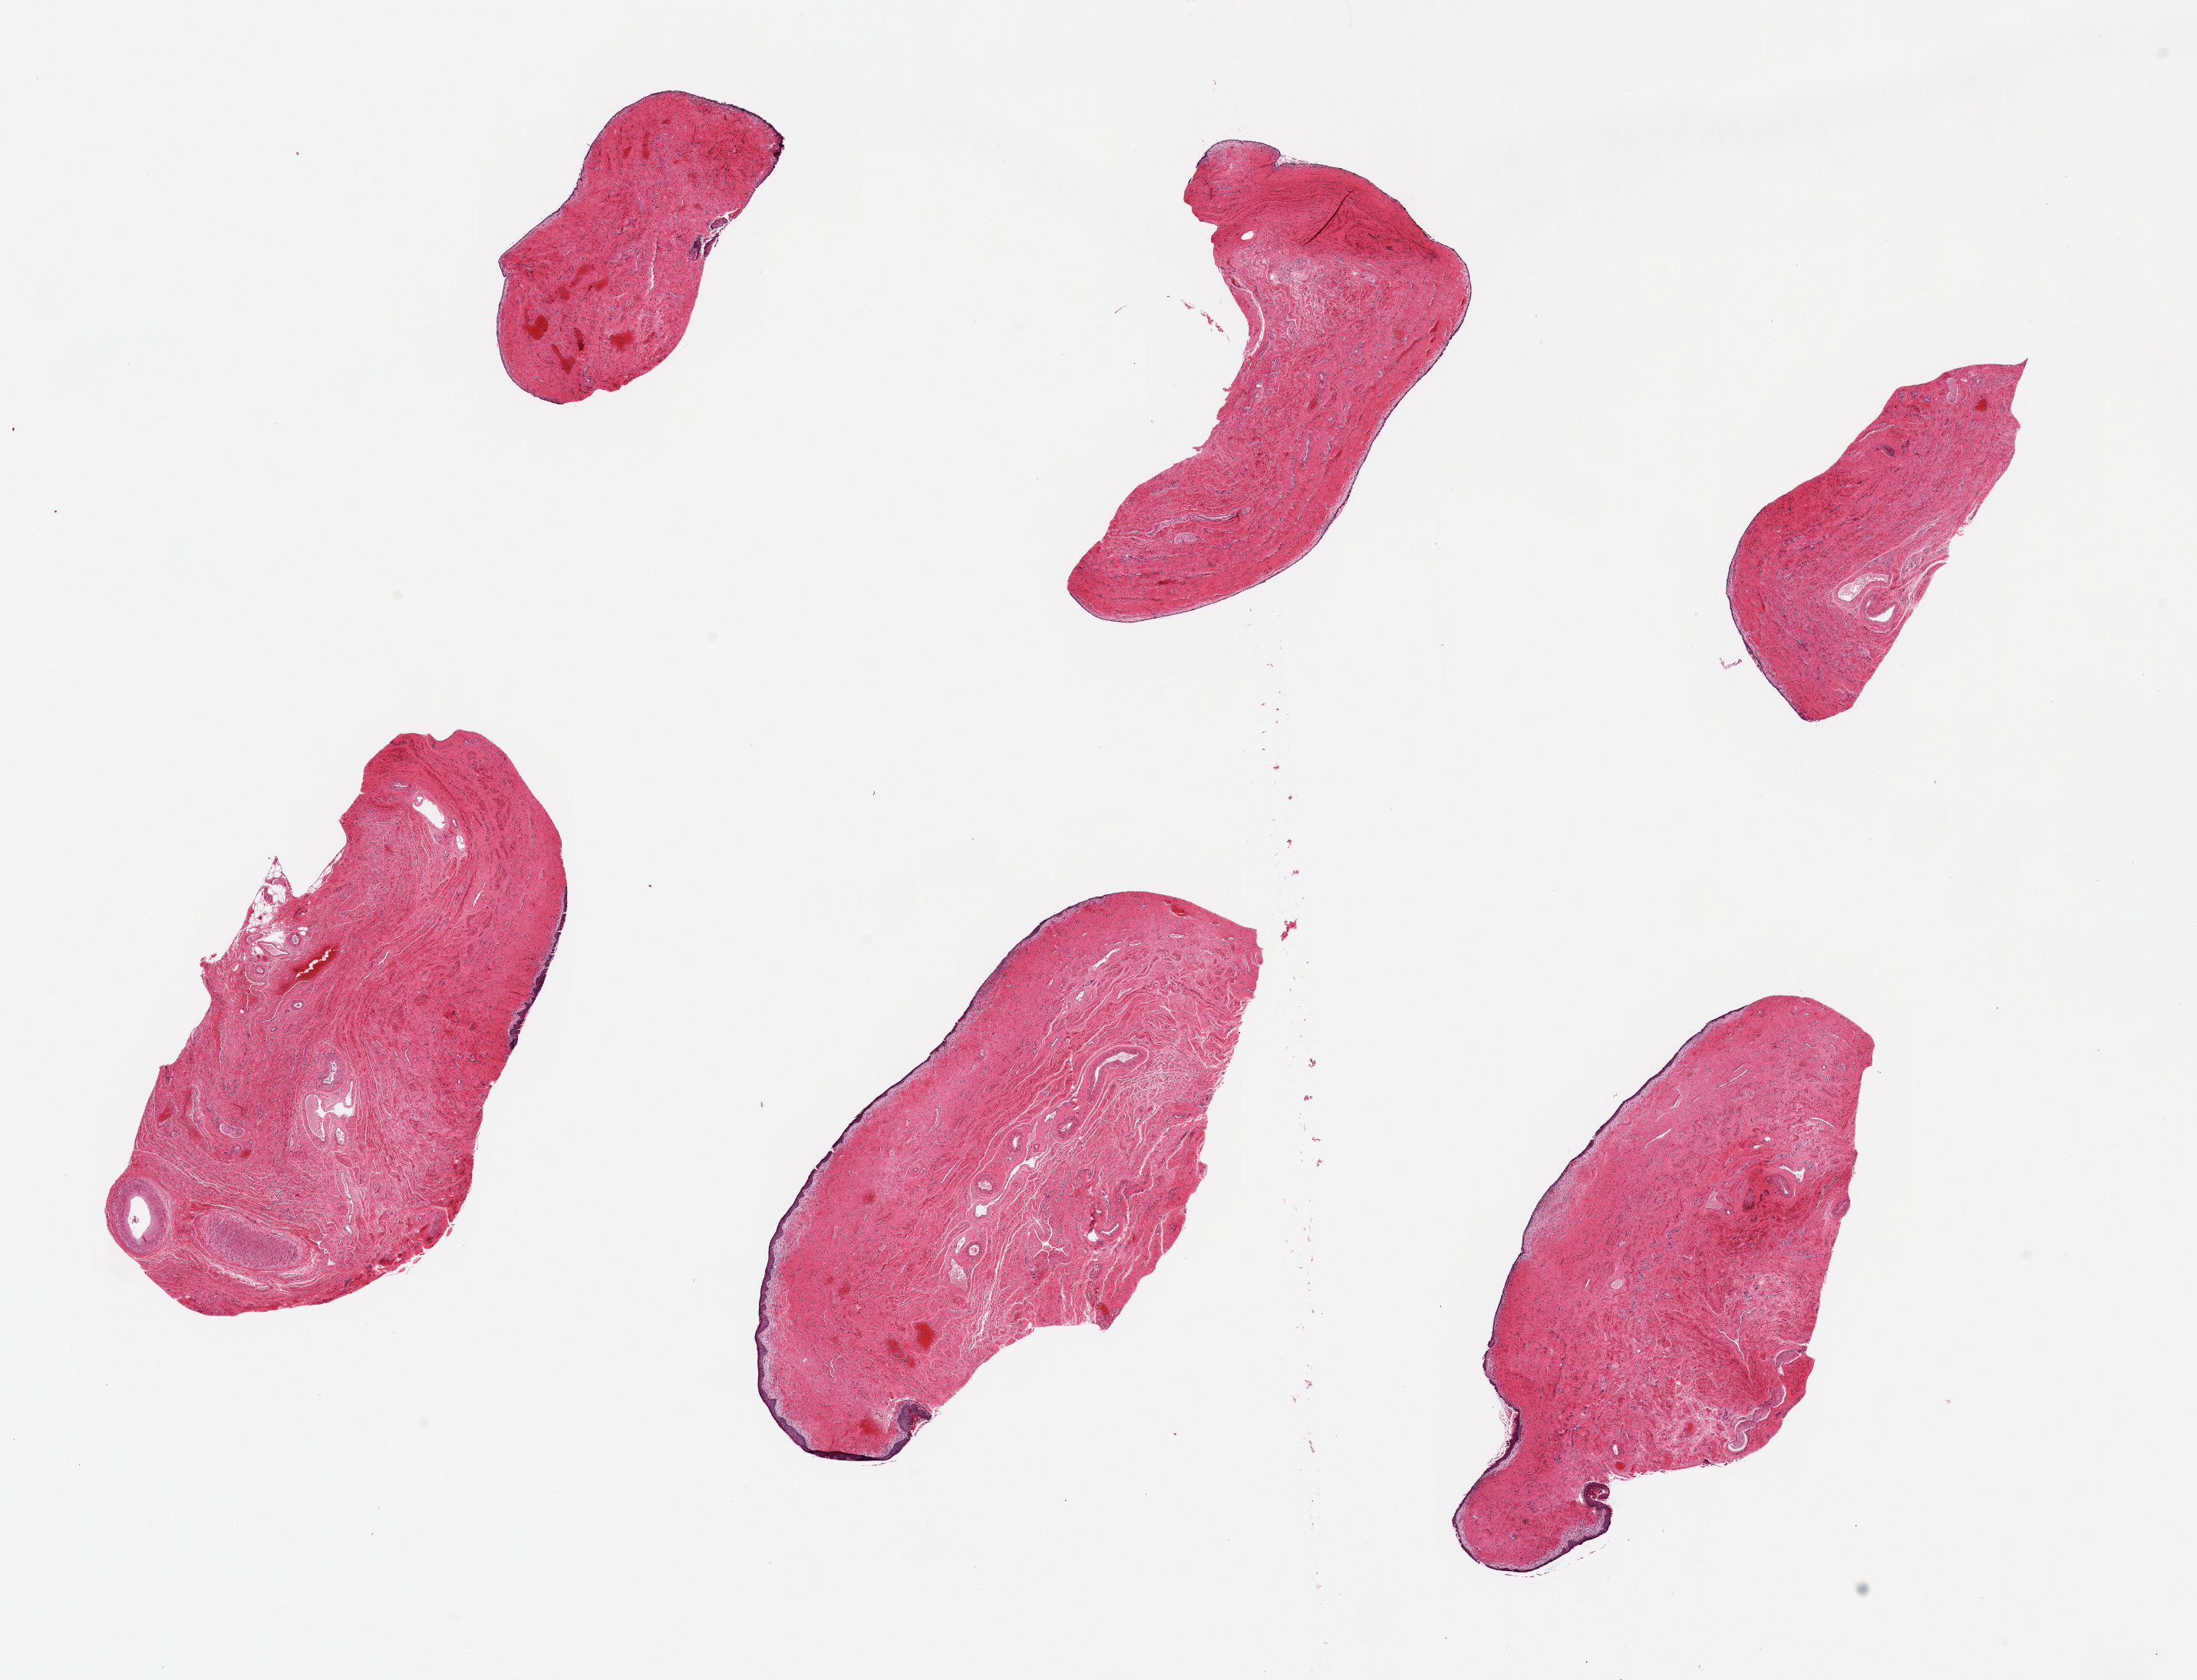
Digitized H&E-stained section, a low-resolution overview of the entire scanned area, about 22.6 x 17.3 mm. PAXgene-fixed, paraffin-embedded tissue. Section of vagina (target tissue). Tissue donor sample. Donor: female.
• review note (as recorded): 6 pieces. up to 7x3mm; largely sloughed epithelium